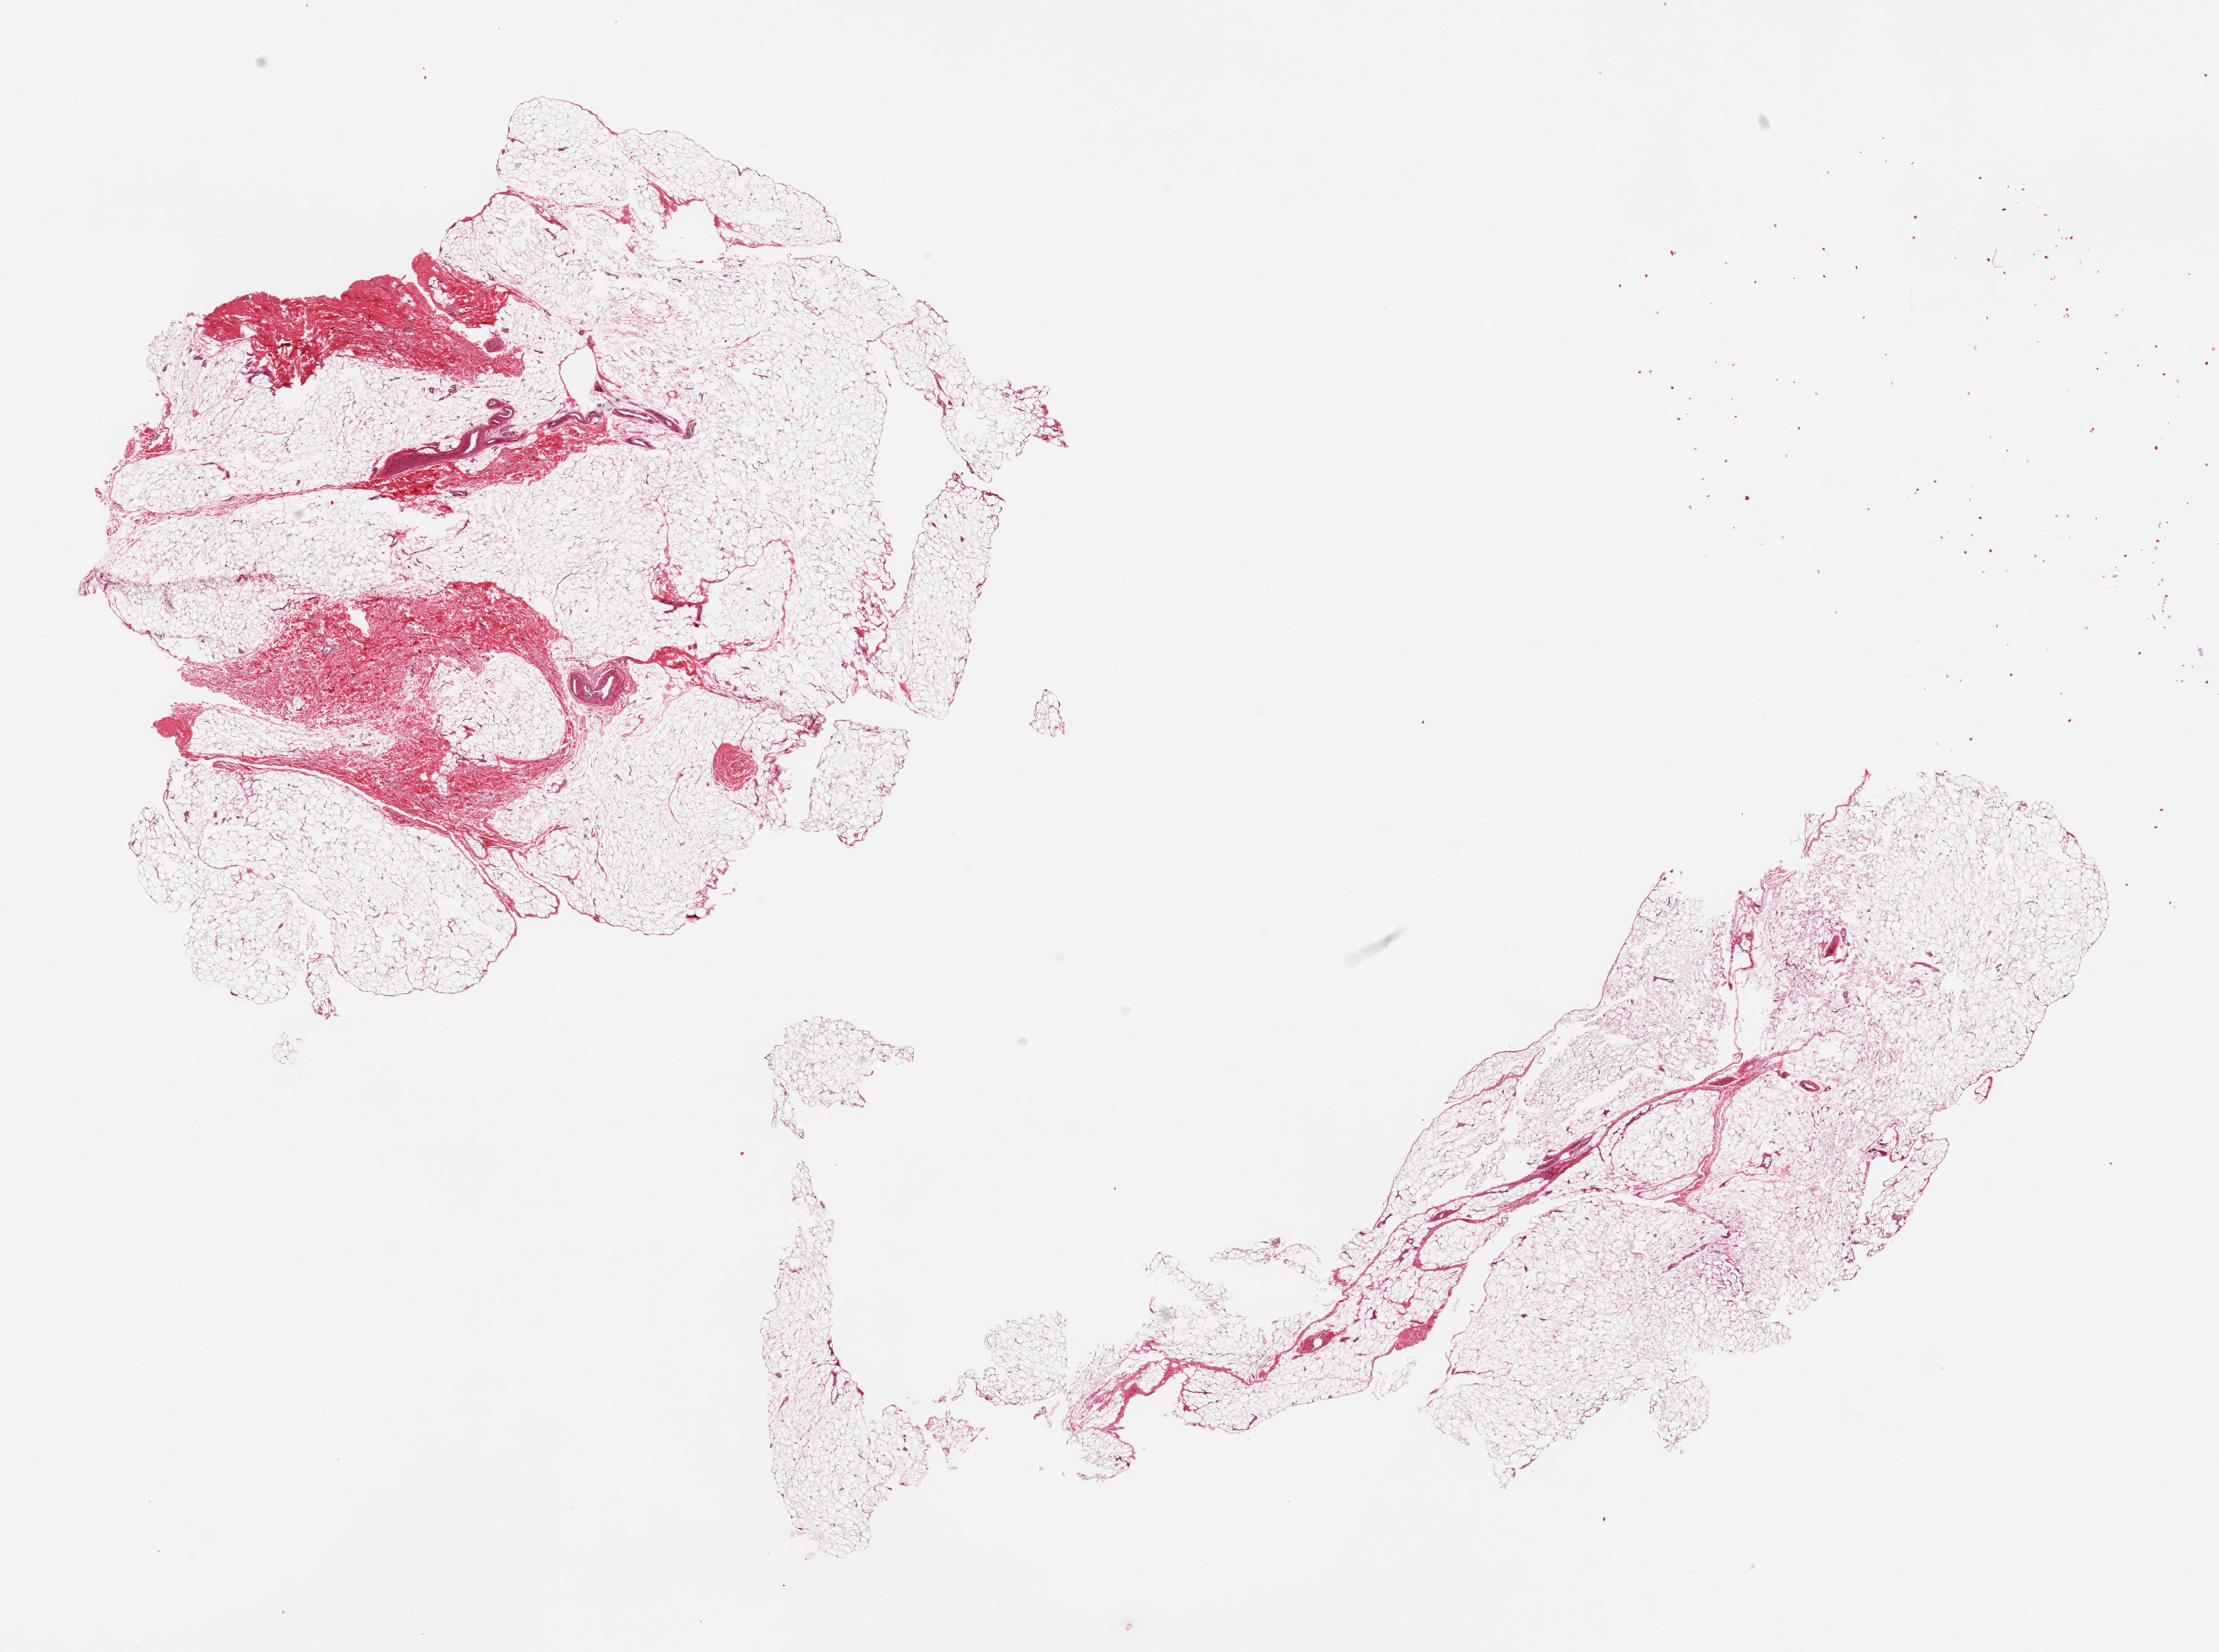
Digitized H&E-stained section, low-resolution overview of the scanned area, about 23.6 x 17.6 mm, PAXgene-fixed, paraffin-embedded tissue, section of adipose tissue (target tissue), tissue donor sample. Donor sex: male.
Pathologist's review note for this sample: 2 pieces, fascia/vascular elements are ~10-15%.